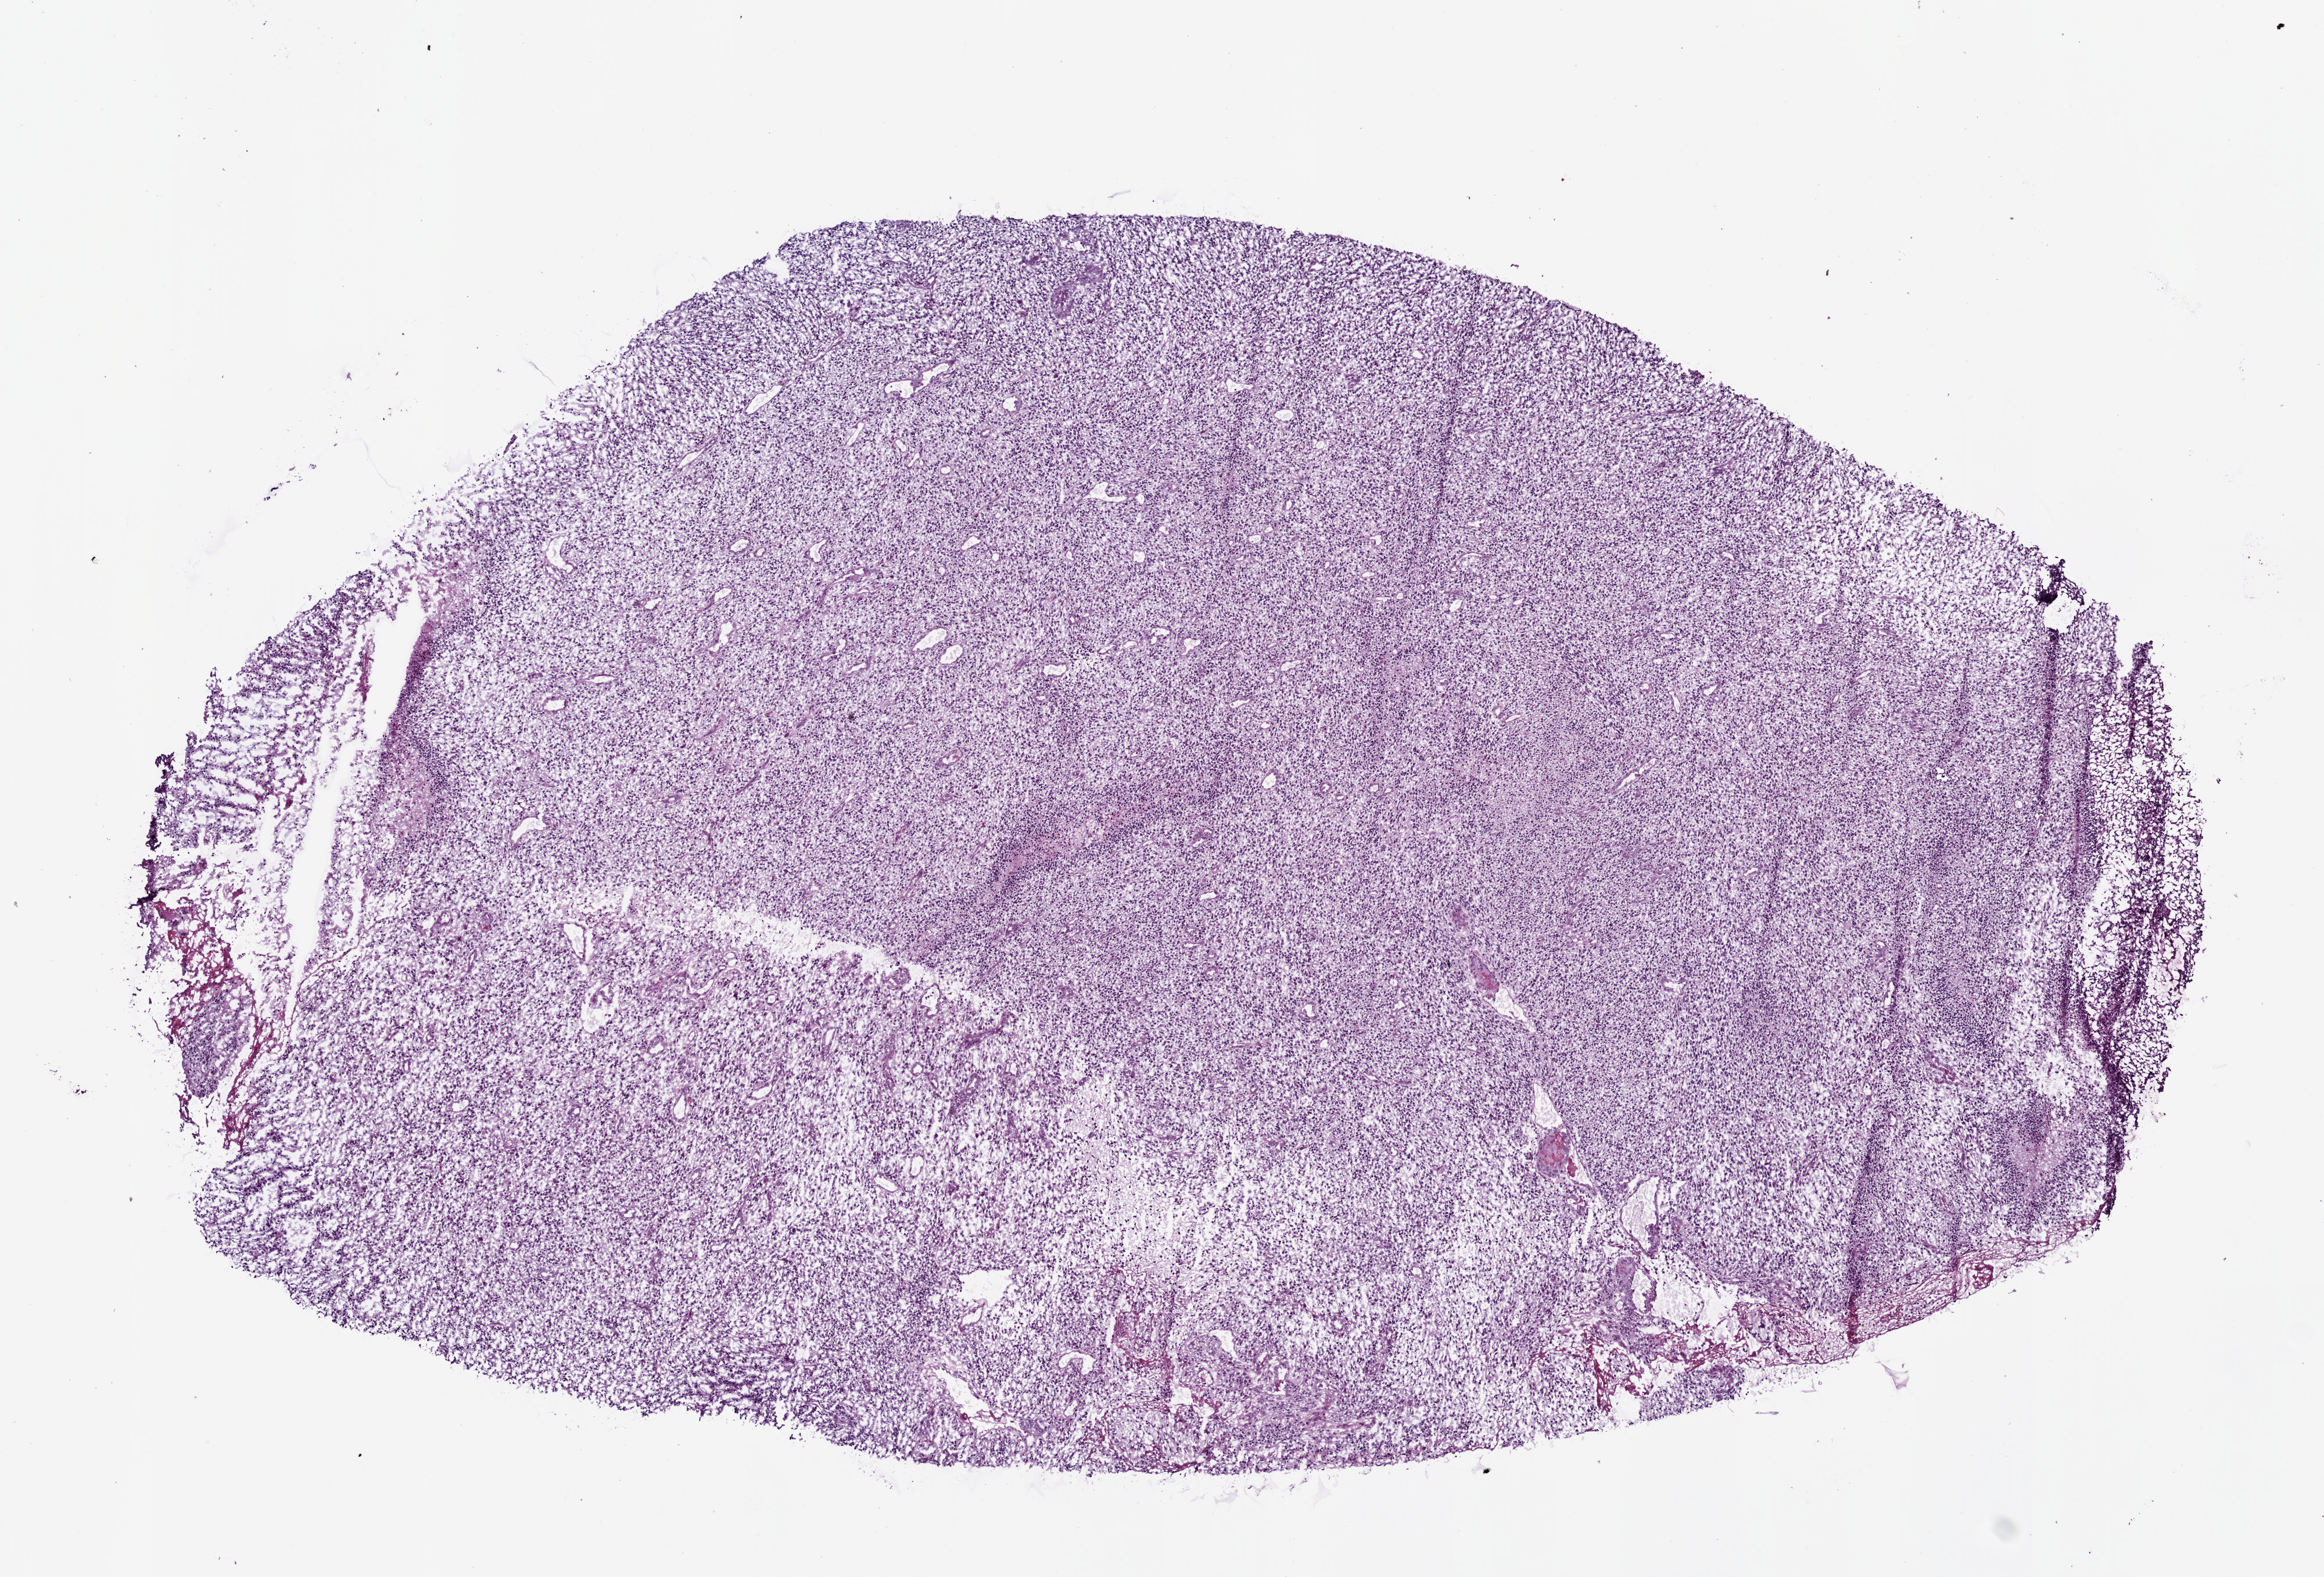
Digitized H&E-stained tissue section (whole slide), shown as a low-resolution overview of the whole scanned area (about 8.0 x 5.4 mm, acquisition: 20x scan). Frozen section. Brain, primary tumour sample. Female patient; age at initial diagnosis 66 years.
Diagnosis: Glioblastoma.